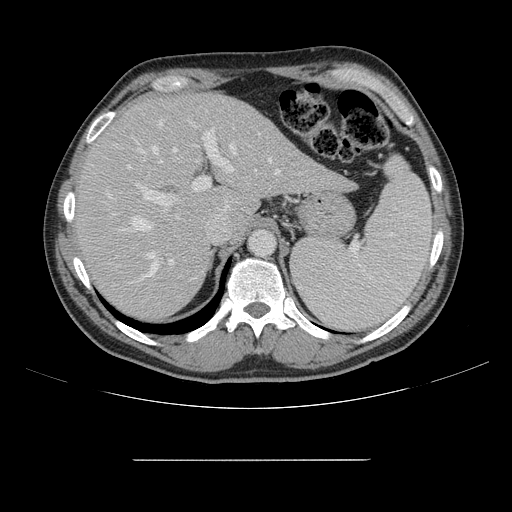
Contrast-enhanced abdominal CT, one axial slice; position 109 of 164 along the scan axis; intravenous contrast given; soft-tissue window (W 400 / L 40 HU); 2.5 mm slice thickness; 512 × 512 image matrix. Male patient, age 54 years. Case-level facts recorded for this patient, not image findings: diagnosis: colorectal cancer liver metastases, imaged before liver resection; multiple liver metastases: yes.
Annotated regions visible in this slice (expert manual segmentation):
- hepatic veins: box from (x=108, y=123) to (x=280, y=281) px
- liver: (x=76, y=95)–(x=349, y=320)
- planned liver remnant (the part of the liver to remain after resection): (x=77, y=95)–(x=242, y=320)
- portal vein (with intrahepatic branches): (x=127, y=121)–(x=233, y=285)